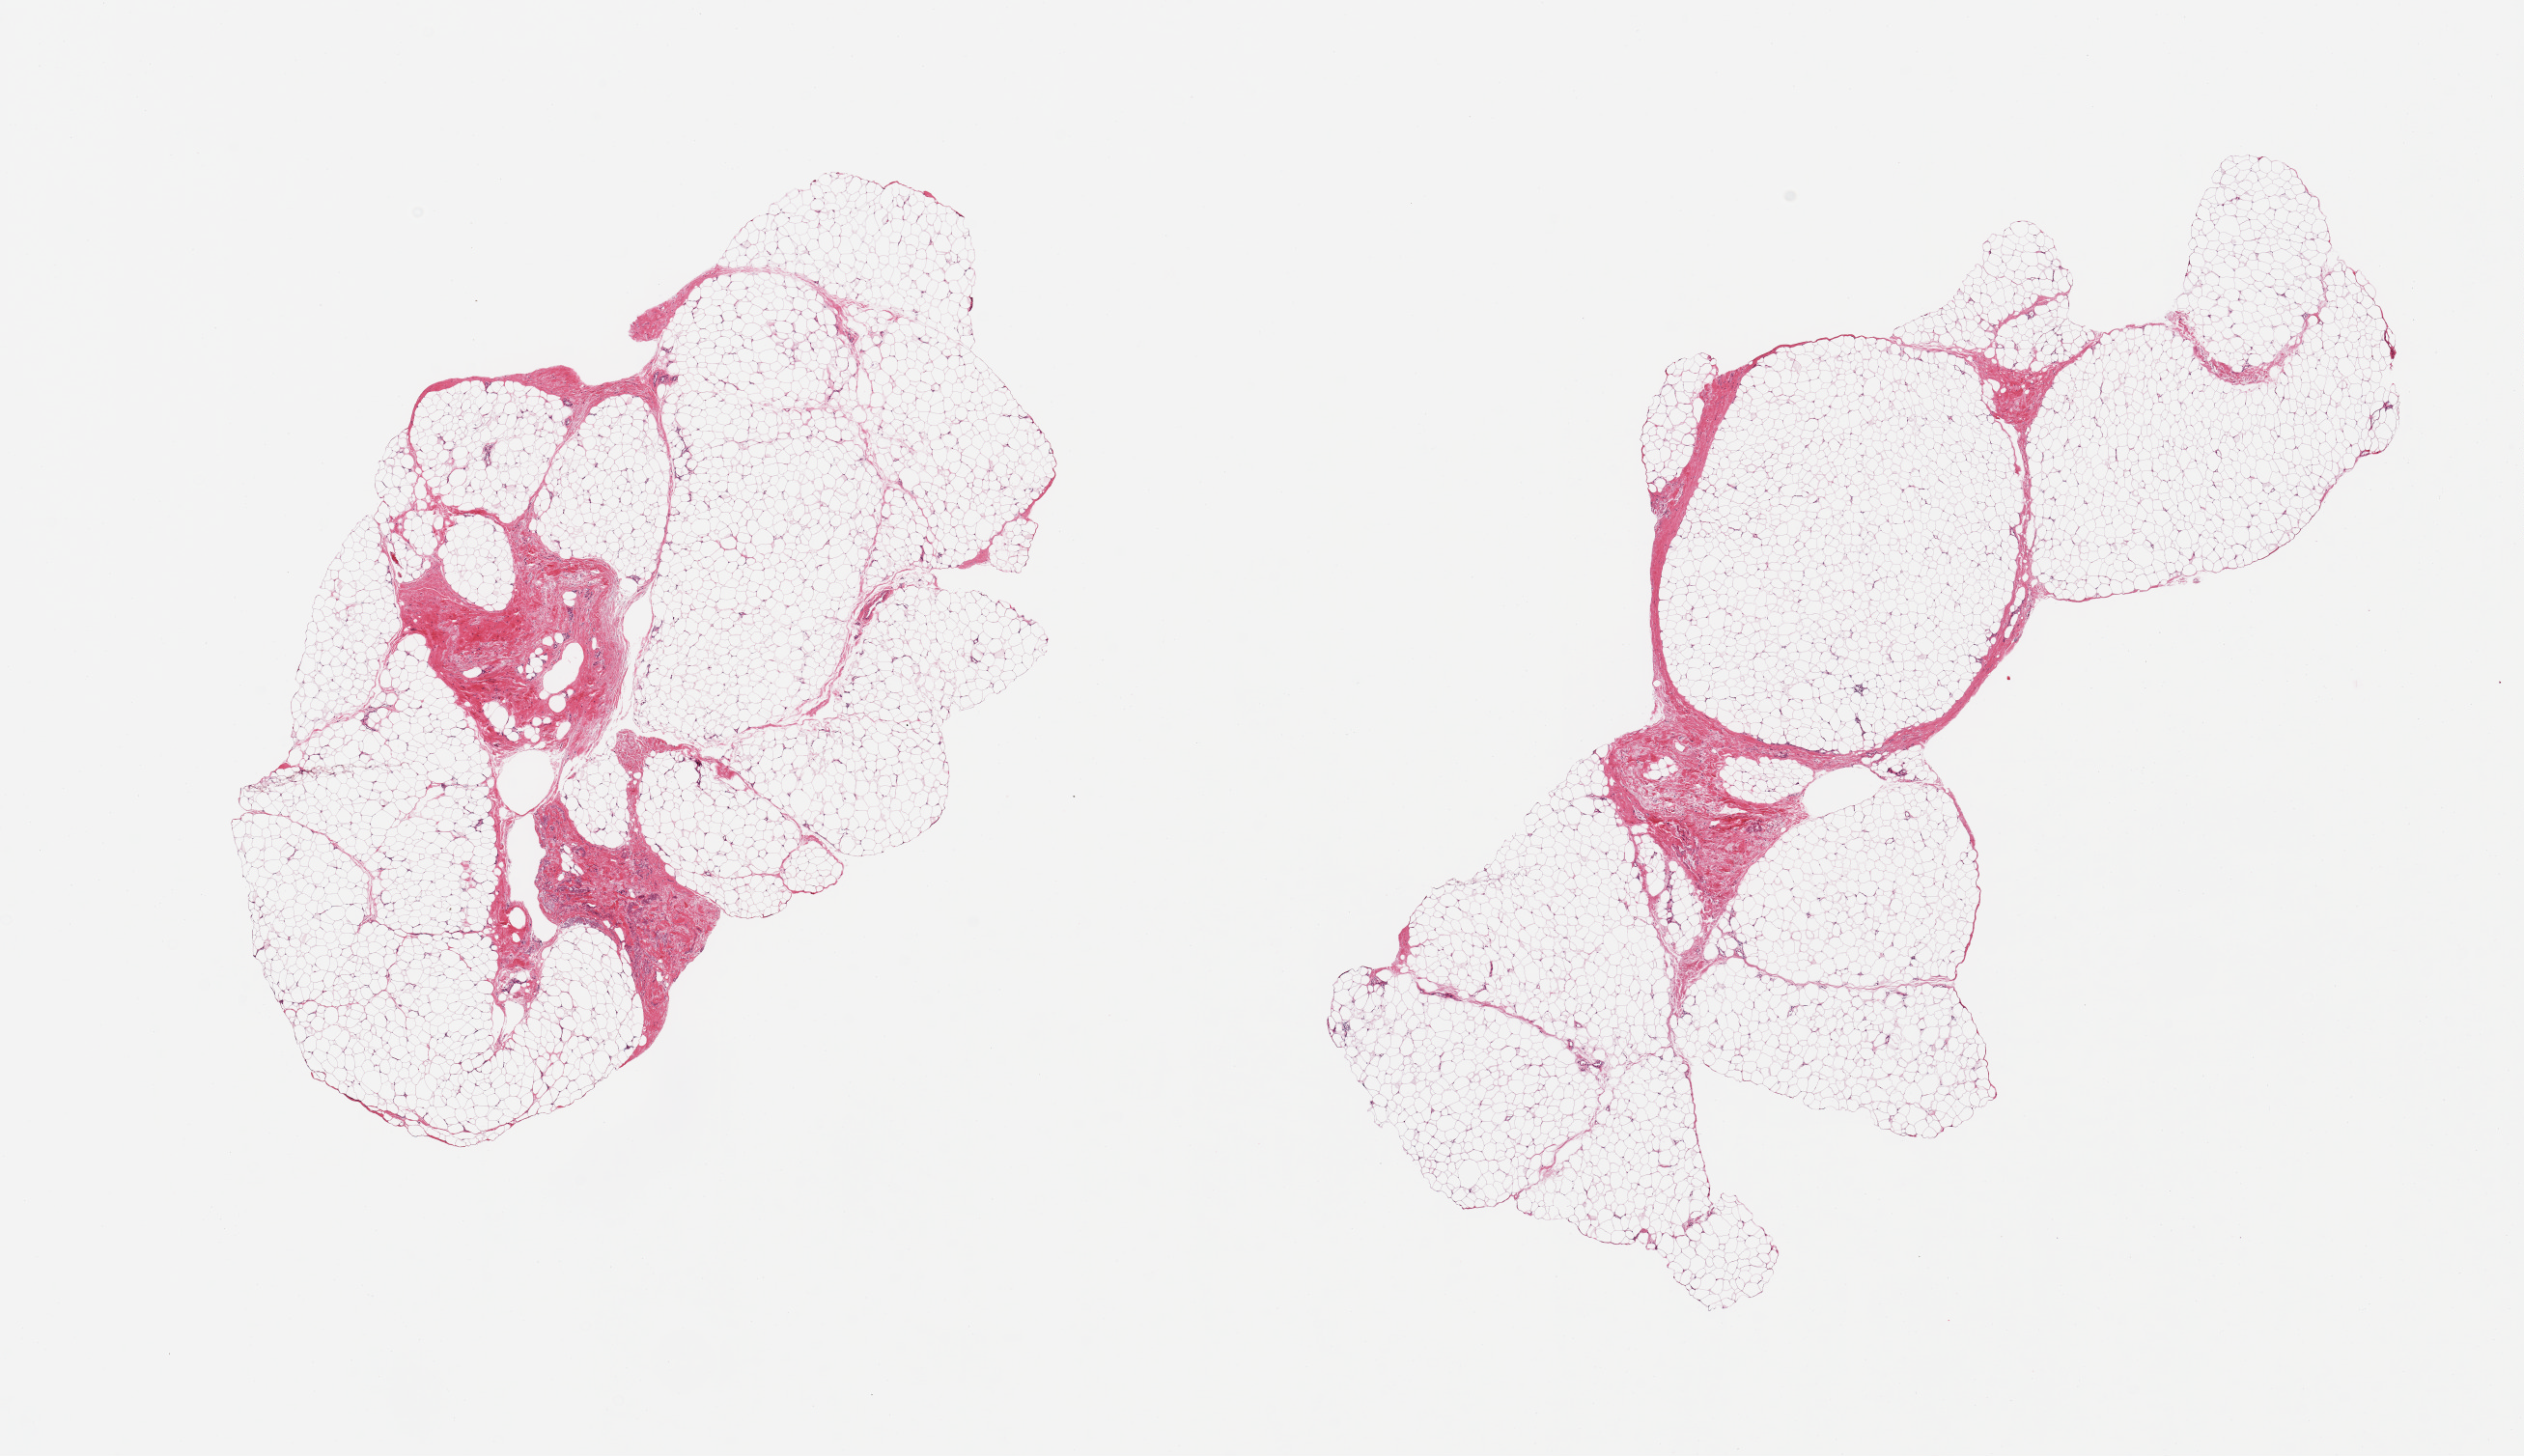
Whole-slide image, H&E stain, whole scanned area (about 20.7 x 11.9 mm, from a 20x scan) shown as a low-resolution overview, PAXgene-fixed, paraffin-embedded tissue, sampled site (target tissue): adipose tissue, tissue donor sample.
Review note (as recorded): 2 pieces; mature fat with 10-15% fibrous component.